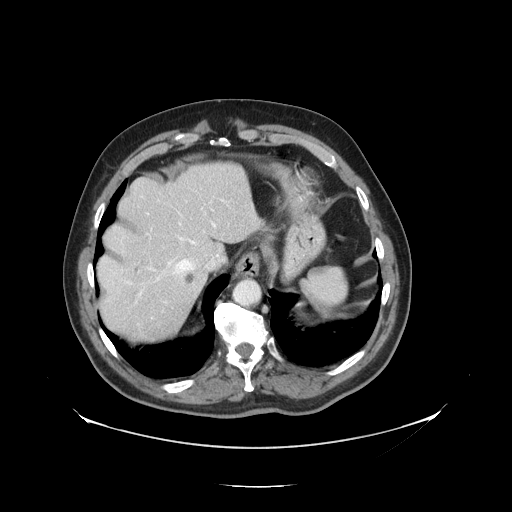
Contrast-enhanced abdominal CT, one axial slice. Slice 110 of 138 in the series (ordered by position). Reconstruction kernel STANDARD. 120 kVp. Intravenous contrast given. Soft-tissue window (W 400 / L 40 HU). 2.5 mm slice thickness. 512 × 512 image matrix. Male patient, age 77 years. From the clinical record (not read from this slice): diagnosis: colorectal cancer liver metastases, imaged before liver resection; multiple liver metastases: no; largest metastasis: 1.5 cm; disease in both lobes: no.
Annotated regions visible in this slice (manually delineated by an expert):
- hepatic veins: bounding box (x1, y1, x2, y2) in pixels: (141, 201, 217, 286)
- liver: (98, 164, 257, 341)
- planned liver remnant (the part of the liver to remain after resection): (98, 164, 257, 289)
- portal vein (with intrahepatic branches): (147, 187, 228, 319)
- liver metastasis: (186, 276, 195, 283)